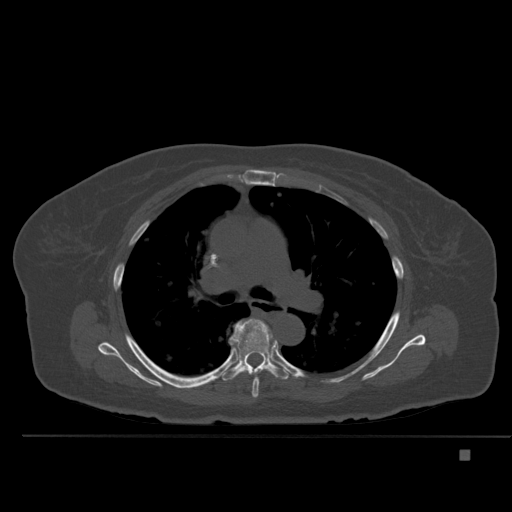
CT including the spine, one axial slice. Slice 345 of 477 in the series (ordered by position). Bone window (W 1800 / L 400 HU). 512 × 512 image matrix. Patient: female, 74 years. Case-level facts recorded for this patient, not image findings: primary cancer: colon.
Outlined on this slice (semi-automatic segmentation, software-assisted and operator-edited):
- T5 vertebra: bounding box <252,373,259,399> (left, top, right, bottom; pixels)
- T6 vertebra: <221,318,290,381>